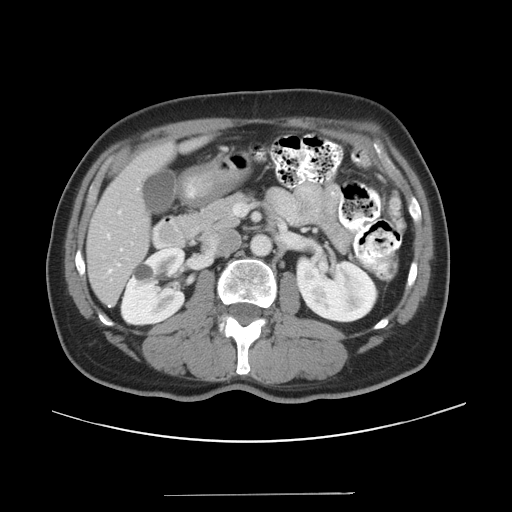
Contrast-enhanced abdominal CT, one axial slice; position 15 of 43 along the scan axis; intravenous contrast given; soft-tissue window (W 400 / L 40 HU); 5 mm slice thickness; 512 × 512 image matrix. Male patient, age 65 years. From the clinical record (not read from this slice): diagnosis: colorectal cancer liver metastases, imaged before liver resection; multiple liver metastases: no.
Outlined on this slice (manually delineated by an expert):
- hepatic veins: bounding box [x1, y1, x2, y2] px = [107, 235, 122, 273]
- liver: [87, 140, 202, 304]
- planned liver remnant (the part of the liver to remain after resection): [87, 139, 204, 304]